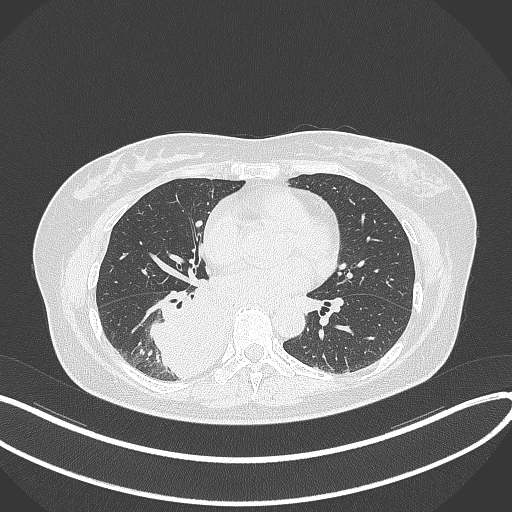
Chest CT, one axial slice. Slice 164 of 331 in the series (ordered by position). 120 kVp. Lung window (W 1500 / L -600 HU). 1 mm slice thickness. 512 × 512 image matrix. Female patient, age 54 years. Case-level facts recorded for this patient, not image findings: clinical TNM (as recorded): T4 N0 M0.
Outlined on this slice (bounding box drawn by a radiologist):
- lung tumour (recorded histology: adenocarcinoma): bounding box [x1, y1, x2, y2] px = [146, 285, 227, 385]